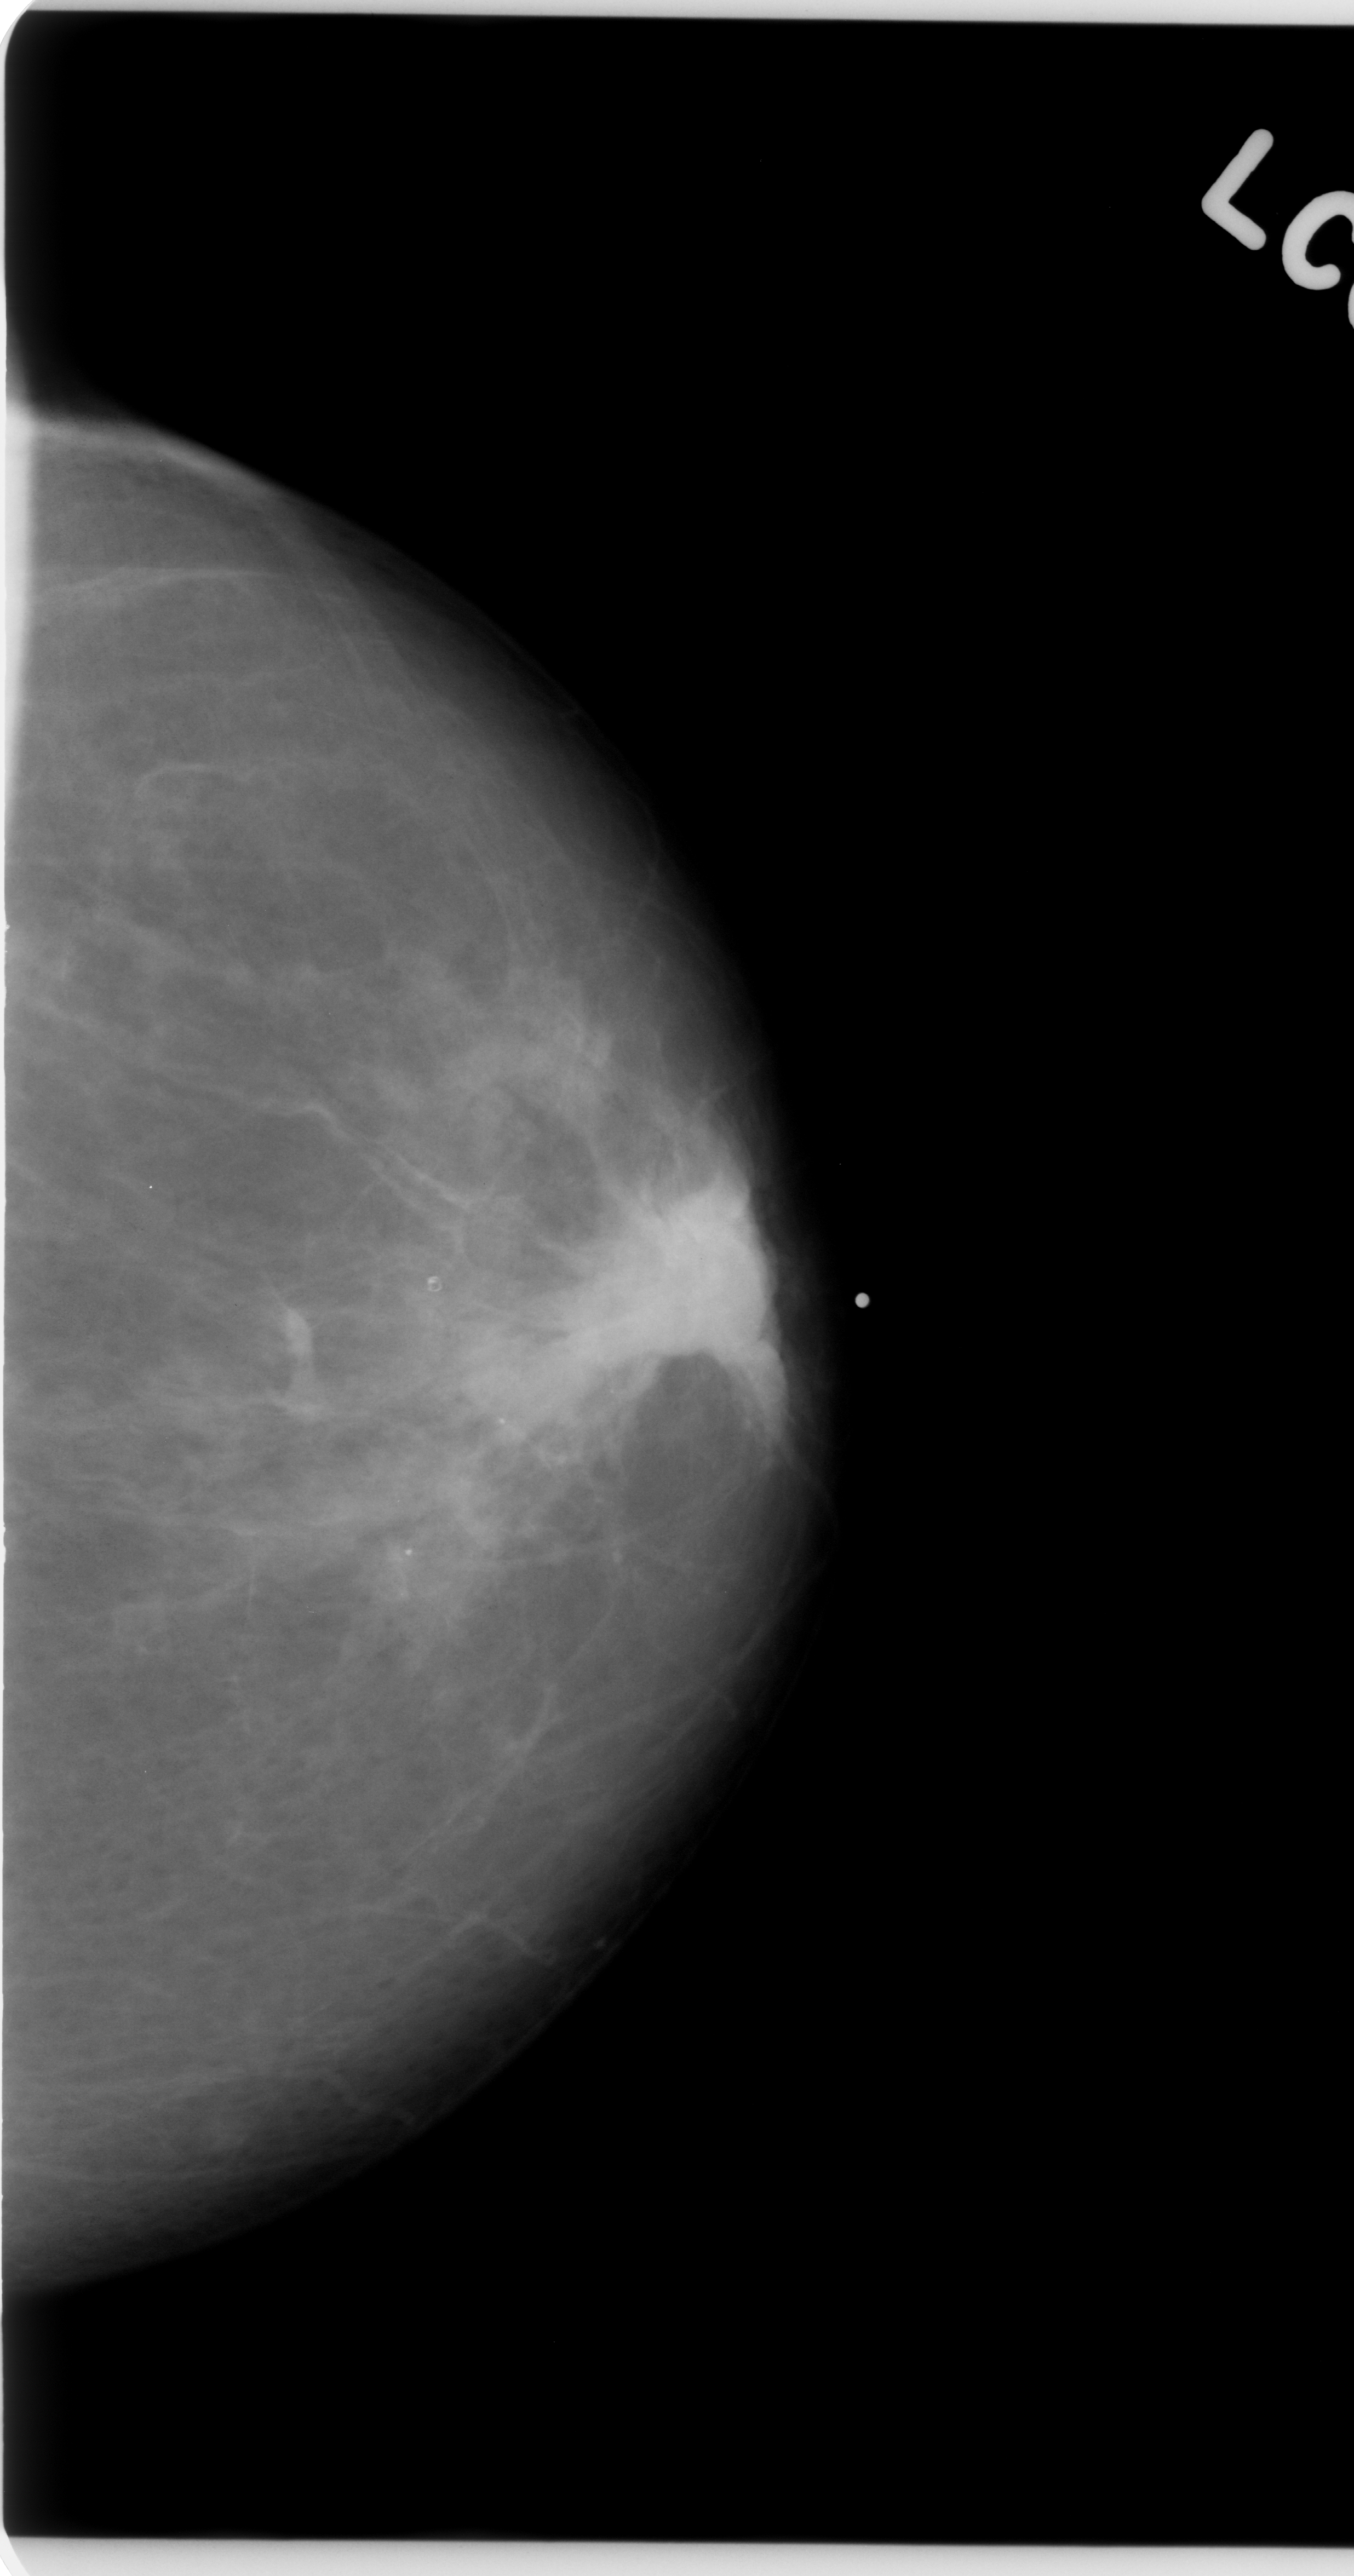
Digitized screen-film mammogram; left breast; craniocaudal (CC) view; breast composition: scattered fibroglandular densities (BI-RADS density category 2 of 4).
Abnormality record for this image: mass, shape irregular, margins spiculated; BI-RADS assessment category 5; subtlety rating 5 on a 1 (subtle) to 5 (obvious) scale; pathology result (as recorded, not read from the image): malignant.